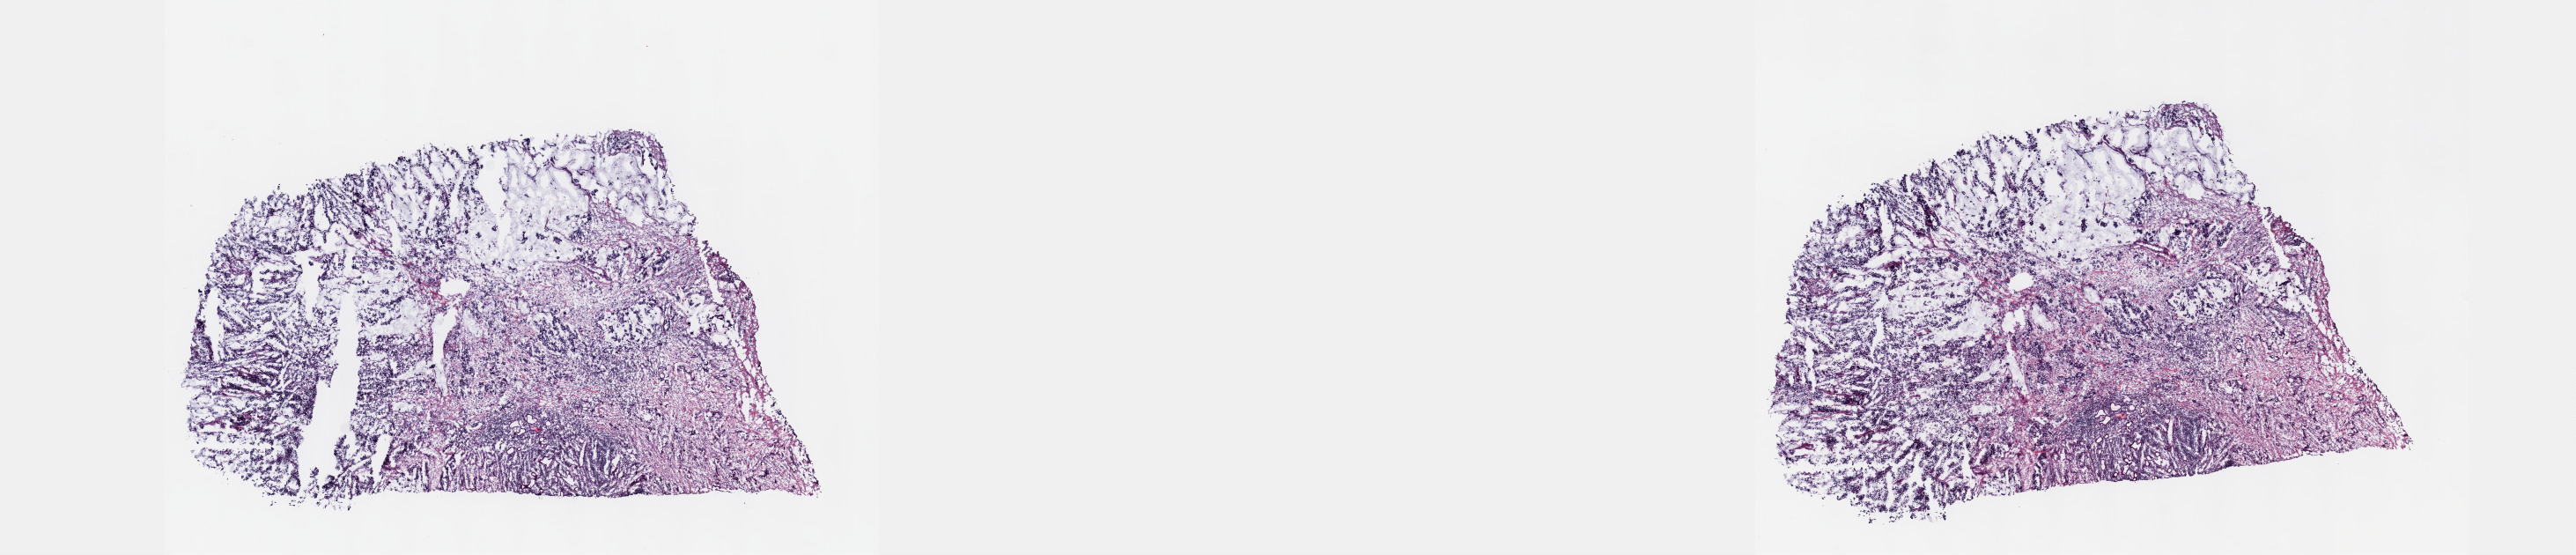
Whole-slide histology image, Hematoxylin and eosin (H&E) stained — shown as a low-resolution overview of the whole scanned area (about 23.6 x 5.1 mm, from a 40x scan). Frozen section from the top of the tissue portion. Esophagus, primary tumour sample. Patient: male, age at initial diagnosis 74 years. Histologic grade: G3 (poorly differentiated). Composition of this section per pathologist review: tumour cells 55%, tumour nuclei 70%, normal cells 0%, stromal cells 40%, necrosis 5%. Inflammatory infiltration, as recorded: lymphocyte infiltration 25%, monocyte infiltration 1%, neutrophil infiltration 3%.
Lymph nodes positive (case pathology): 2 of 7 examined. Pathologic diagnosis: Adenocarcinoma, NOS (lower third of esophagus). AJCC pathologic stage: III (5th edition).